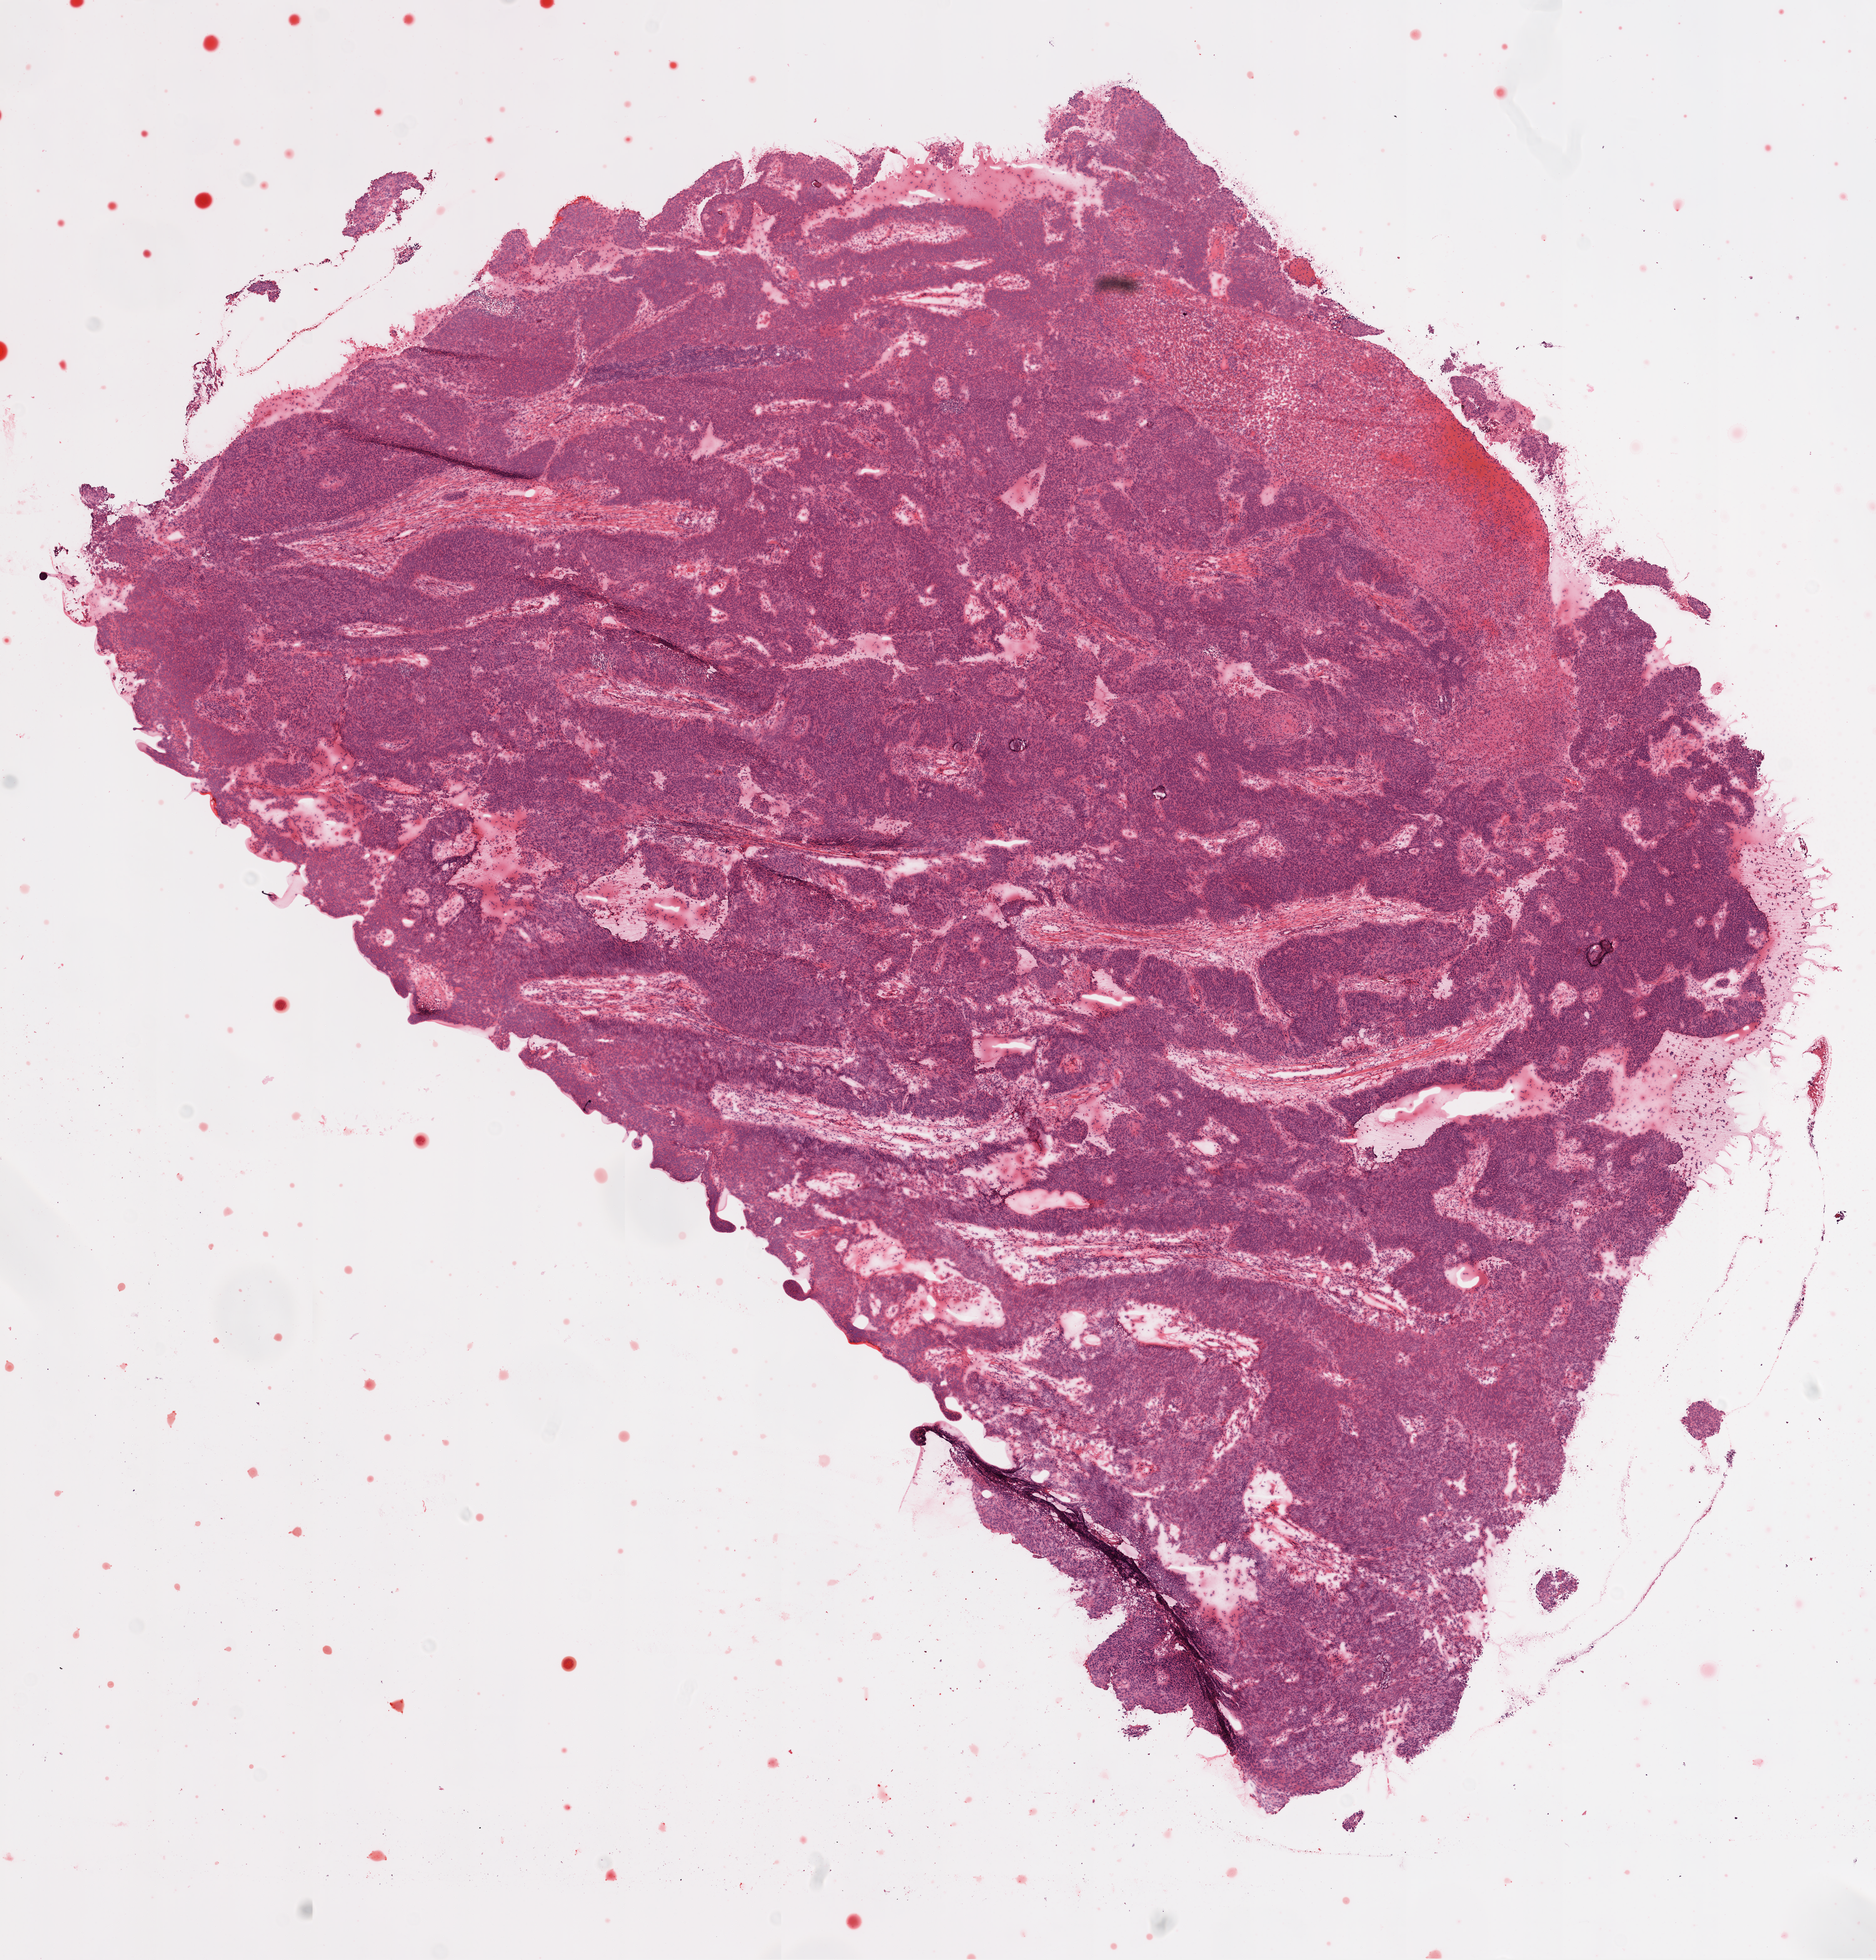
H&E whole-slide image, a low-resolution overview of the entire scanned area, about 12.0 x 12.6 mm; frozen section from the top of the tissue portion; ovary, primary tumour sample. Female patient; age at initial diagnosis 50 years. Histologic grade: G3 (poorly differentiated). Slide review estimates, as recorded: tumour cells 94%, tumour nuclei 95%, normal cells 0%, stromal cells 5%, necrosis 1%.
• histologic diagnosis: Serous cystadenocarcinoma, NOS
• FIGO stage: IIC